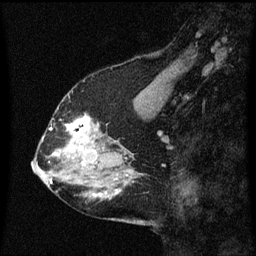
Breast MRI (dynamic contrast-enhanced), one sagittal slice; position 24 of 60 along the scan axis; dynamic contrast-enhanced series, image 2 of 3 at this slice position (ordered by acquisition); 1.5 T; TE 4.2 ms, TR 8.4 ms; 256 × 256 image matrix, field of view 200 × 200 mm. Female patient, age 58 years.
Outlined on this slice (semi-automatically segmented with operator editing):
- analysis volume of interest (the breast-tissue region the enhancement analysis was run in; not a lesion): box from (x=58, y=114) to (x=99, y=151) px
- tumour enhancement mask (voxels above the 70 % enhancement threshold inside the analysis volume of interest): (x=68, y=116)–(x=95, y=151)